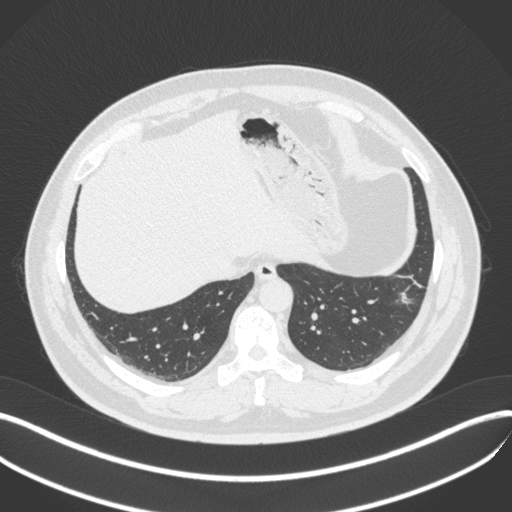
Chest CT, one axial slice; slice 105 of 420 in the series (ordered by position); reconstruction kernel B31f; lung window (W 1500 / L -600 HU); 512 × 512 image matrix, field of view 400 × 400 mm. Patient: male, 39 years. From the clinical record (not read from this slice): clinical TNM (as recorded): T2a N0 M0; histopathological grade: G2-3.
Structures marked on this image (rectangle marked by the reading radiologist):
- lung tumour (recorded histology: adenocarcinoma): bounding box <395,281,415,312> (left, top, right, bottom; pixels)